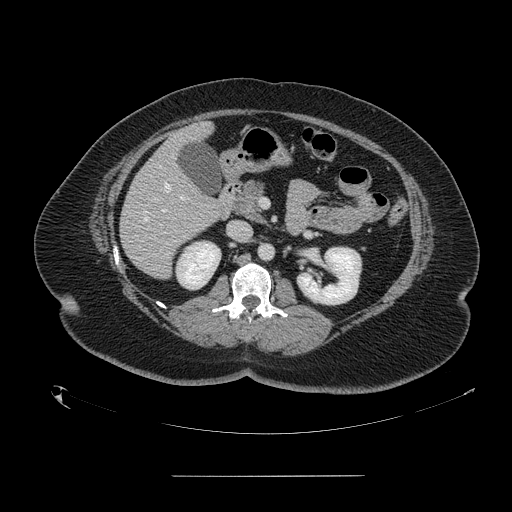
Contrast-enhanced abdominal CT, one axial slice; slice 69 of 164 in the series (ordered by position); 120 kVp; intravenous contrast given; soft-tissue window (W 400 / L 40 HU); 2.5 mm slice thickness; 512 × 512 image matrix, field of view 495 × 495 mm. Female patient, age 52 years. Case-level facts recorded for this patient, not image findings: diagnosis: colorectal cancer liver metastases, imaged before liver resection; multiple liver metastases: yes; largest metastasis: 3.5 cm; chemotherapy before resection: no.
Structures marked on this image (outlined manually by an expert reader):
- hepatic veins: bounding box (x1, y1, x2, y2) in pixels: (144, 183, 170, 221)
- liver: (121, 124, 231, 278)
- planned liver remnant (the part of the liver to remain after resection): (181, 124, 211, 144)
- portal vein (with intrahepatic branches): (180, 196, 184, 199)